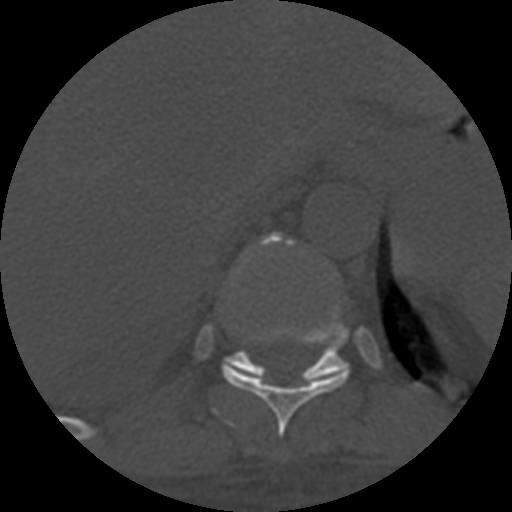
CT including the spine, one axial slice; slice 349 of 708 in the series (ordered by position); 120 kVp; one of 3 acquisitions stored at this slice position; bone window (W 1800 / L 400 HU); 512 × 512 image matrix, field of view 160 × 160 mm. Patient age 55 years. From the clinical record (not read from this slice): primary cancer: colon.
Annotated regions visible in this slice (semi-automatically segmented with operator editing):
- T10 vertebra: bounding box (x1, y1, x2, y2) in pixels: (222, 234, 350, 436)
- T11 vertebra: (223, 306, 350, 385)